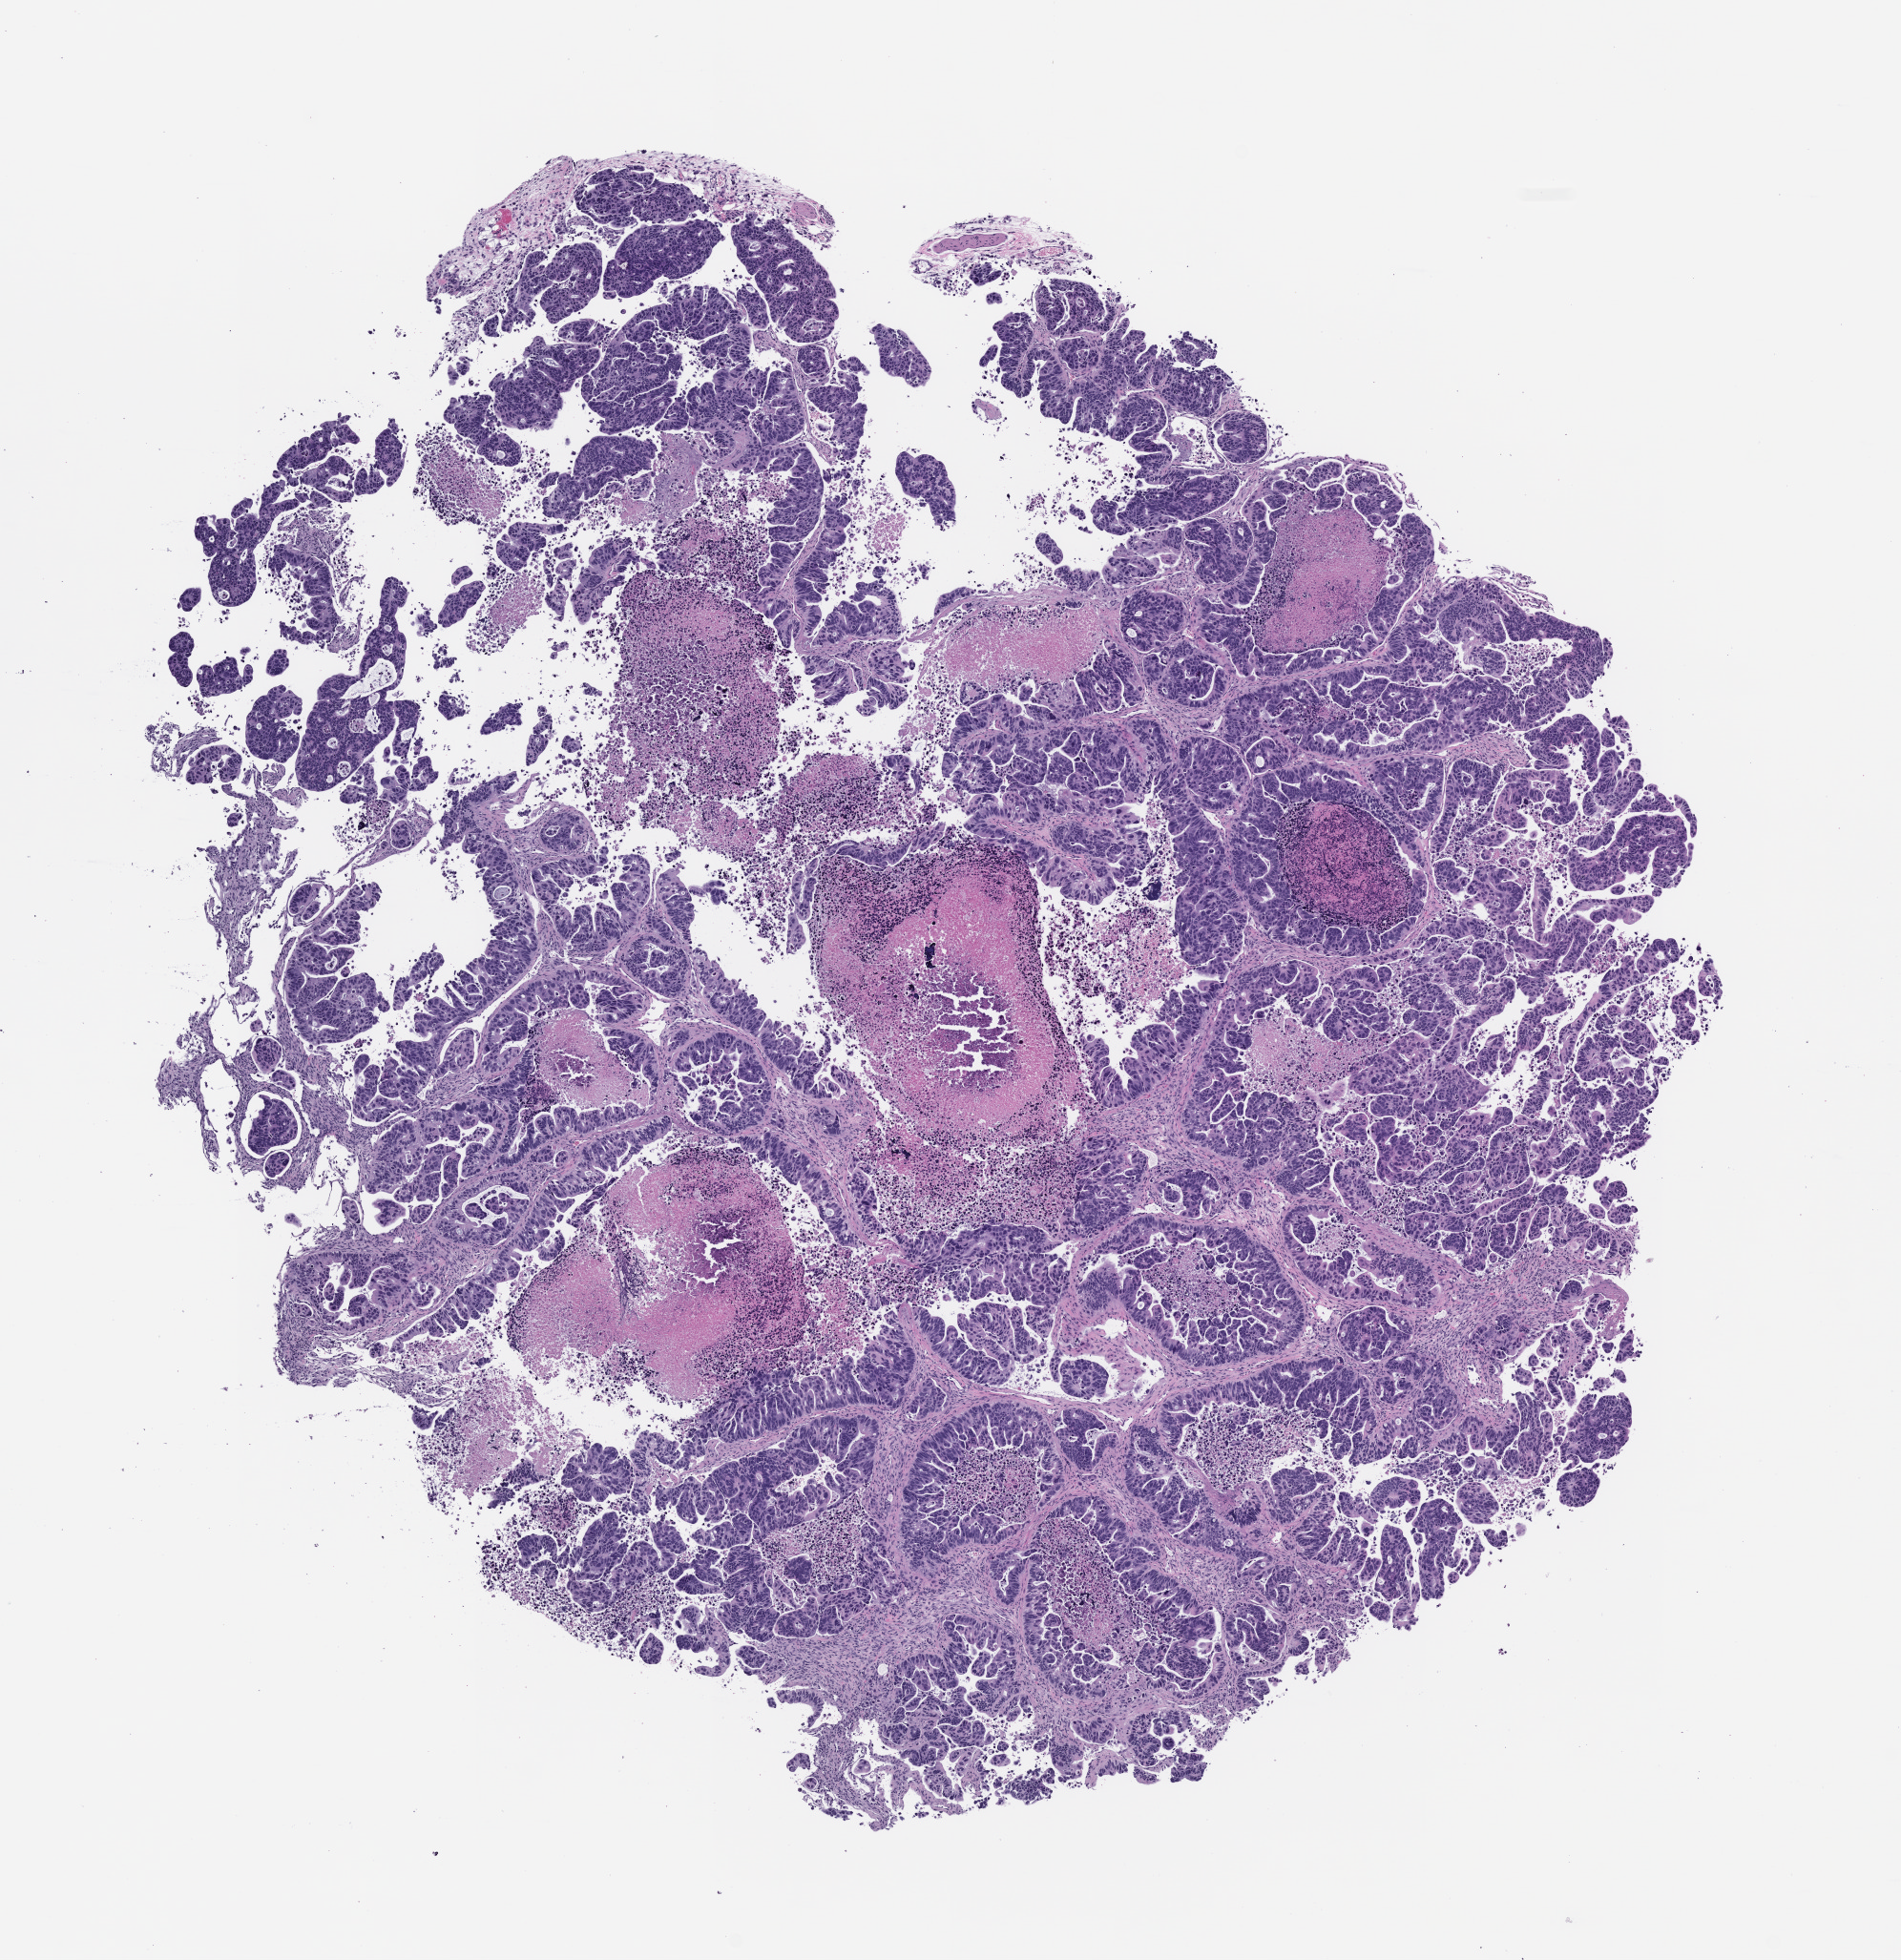
Whole-slide image, H&E: patient-derived xenograft (human tumor grown in a mouse), passage 1, shown as a low-resolution overview of the whole scanned area (about 8.0 x 8.3 mm); FFPE section; tumor site category: colon.
• originating patient diagnosis: Colon Adenocarcinoma